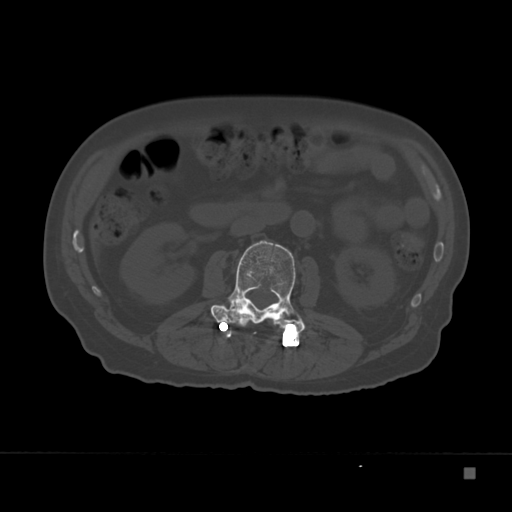
CT including the spine, one axial slice; slice 89 of 332 in the series (ordered by position); bone window (W 1800 / L 400 HU); 512 × 512 image matrix. Patient: male, 72 years. Case-level facts recorded for this patient, not image findings: primary cancer: skeletal.
Annotated regions visible in this slice (semi-automatic segmentation, software-assisted and operator-edited):
- L2 vertebra: bounding box (x1, y1, x2, y2) in pixels: (211, 240, 306, 331)